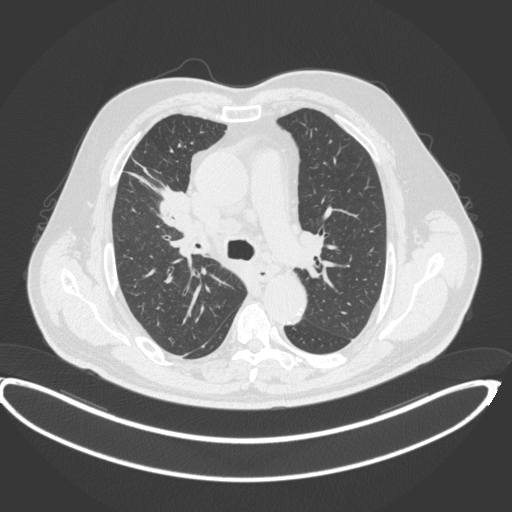
Chest CT, one axial slice. Slice 271 of 395 in the series (ordered by position). Reconstruction kernel B31f. 120 kVp. Lung window (W 1500 / L -600 HU). 512 × 512 image matrix, field of view 448 × 448 mm. Male patient, age 62 years. From the clinical record (not read from this slice): clinical TNM (as recorded): T1c N3 M1c.
Outlined on this slice (bounding box drawn by a radiologist):
- lung tumour (recorded histology: adenocarcinoma): box from (x=152, y=179) to (x=192, y=231) px